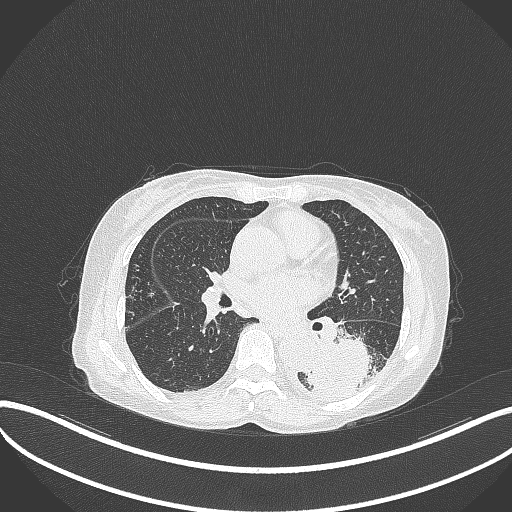
Chest CT, one axial slice; position 157 of 370 along the scan axis; reconstruction kernel B70f; 120 kVp; lung window (W 1500 / L -600 HU); 1 mm slice thickness; 512 × 512 image matrix, field of view 400 × 400 mm. Patient: female, 78 years. Case-level facts recorded for this patient, not image findings: clinical TNM (as recorded): T3 N0 M1.
Structures marked on this image (rectangle marked by the reading radiologist):
- lung tumour (recorded histology: squamous cell carcinoma): bounding box (x1, y1, x2, y2) in pixels: (307, 331, 388, 399)